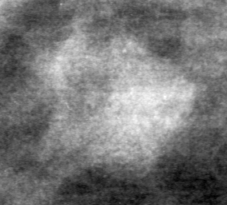
Cropped region of a digitized screen-film mammogram centred on a radiologist-marked abnormality; left breast; MLO view; BI-RADS breast density category 1 (scale 1–4).
Mass, shape lobulated, margins obscured; BI-RADS assessment category 4; subtlety rating 2 on a 1 (subtle) to 5 (obvious) scale; pathology result (as recorded, not read from the image): benign.